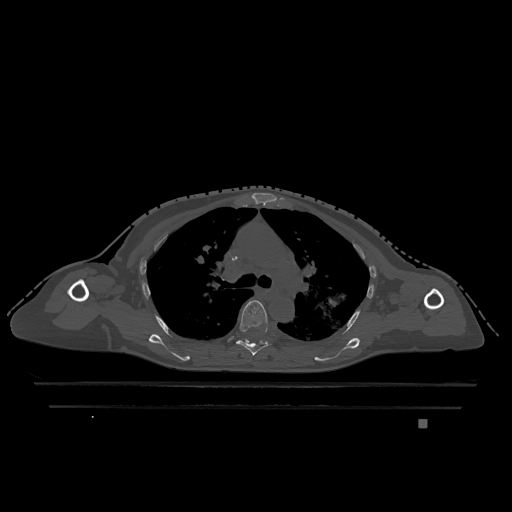
CT including the spine, one axial slice. Position 832 of 1317 along the scan axis. Bone window (W 1800 / L 400 HU). 0.5 mm slice thickness. 512 × 512 image matrix. Patient: female, 74 years. Case-level facts recorded for this patient, not image findings: primary cancer: lung.
Annotated regions visible in this slice (semi-automatic segmentation, software-assisted and operator-edited):
- T5 vertebra: bounding box [x1, y1, x2, y2] px = [236, 300, 271, 356]
- T6 vertebra: [240, 340, 243, 342]